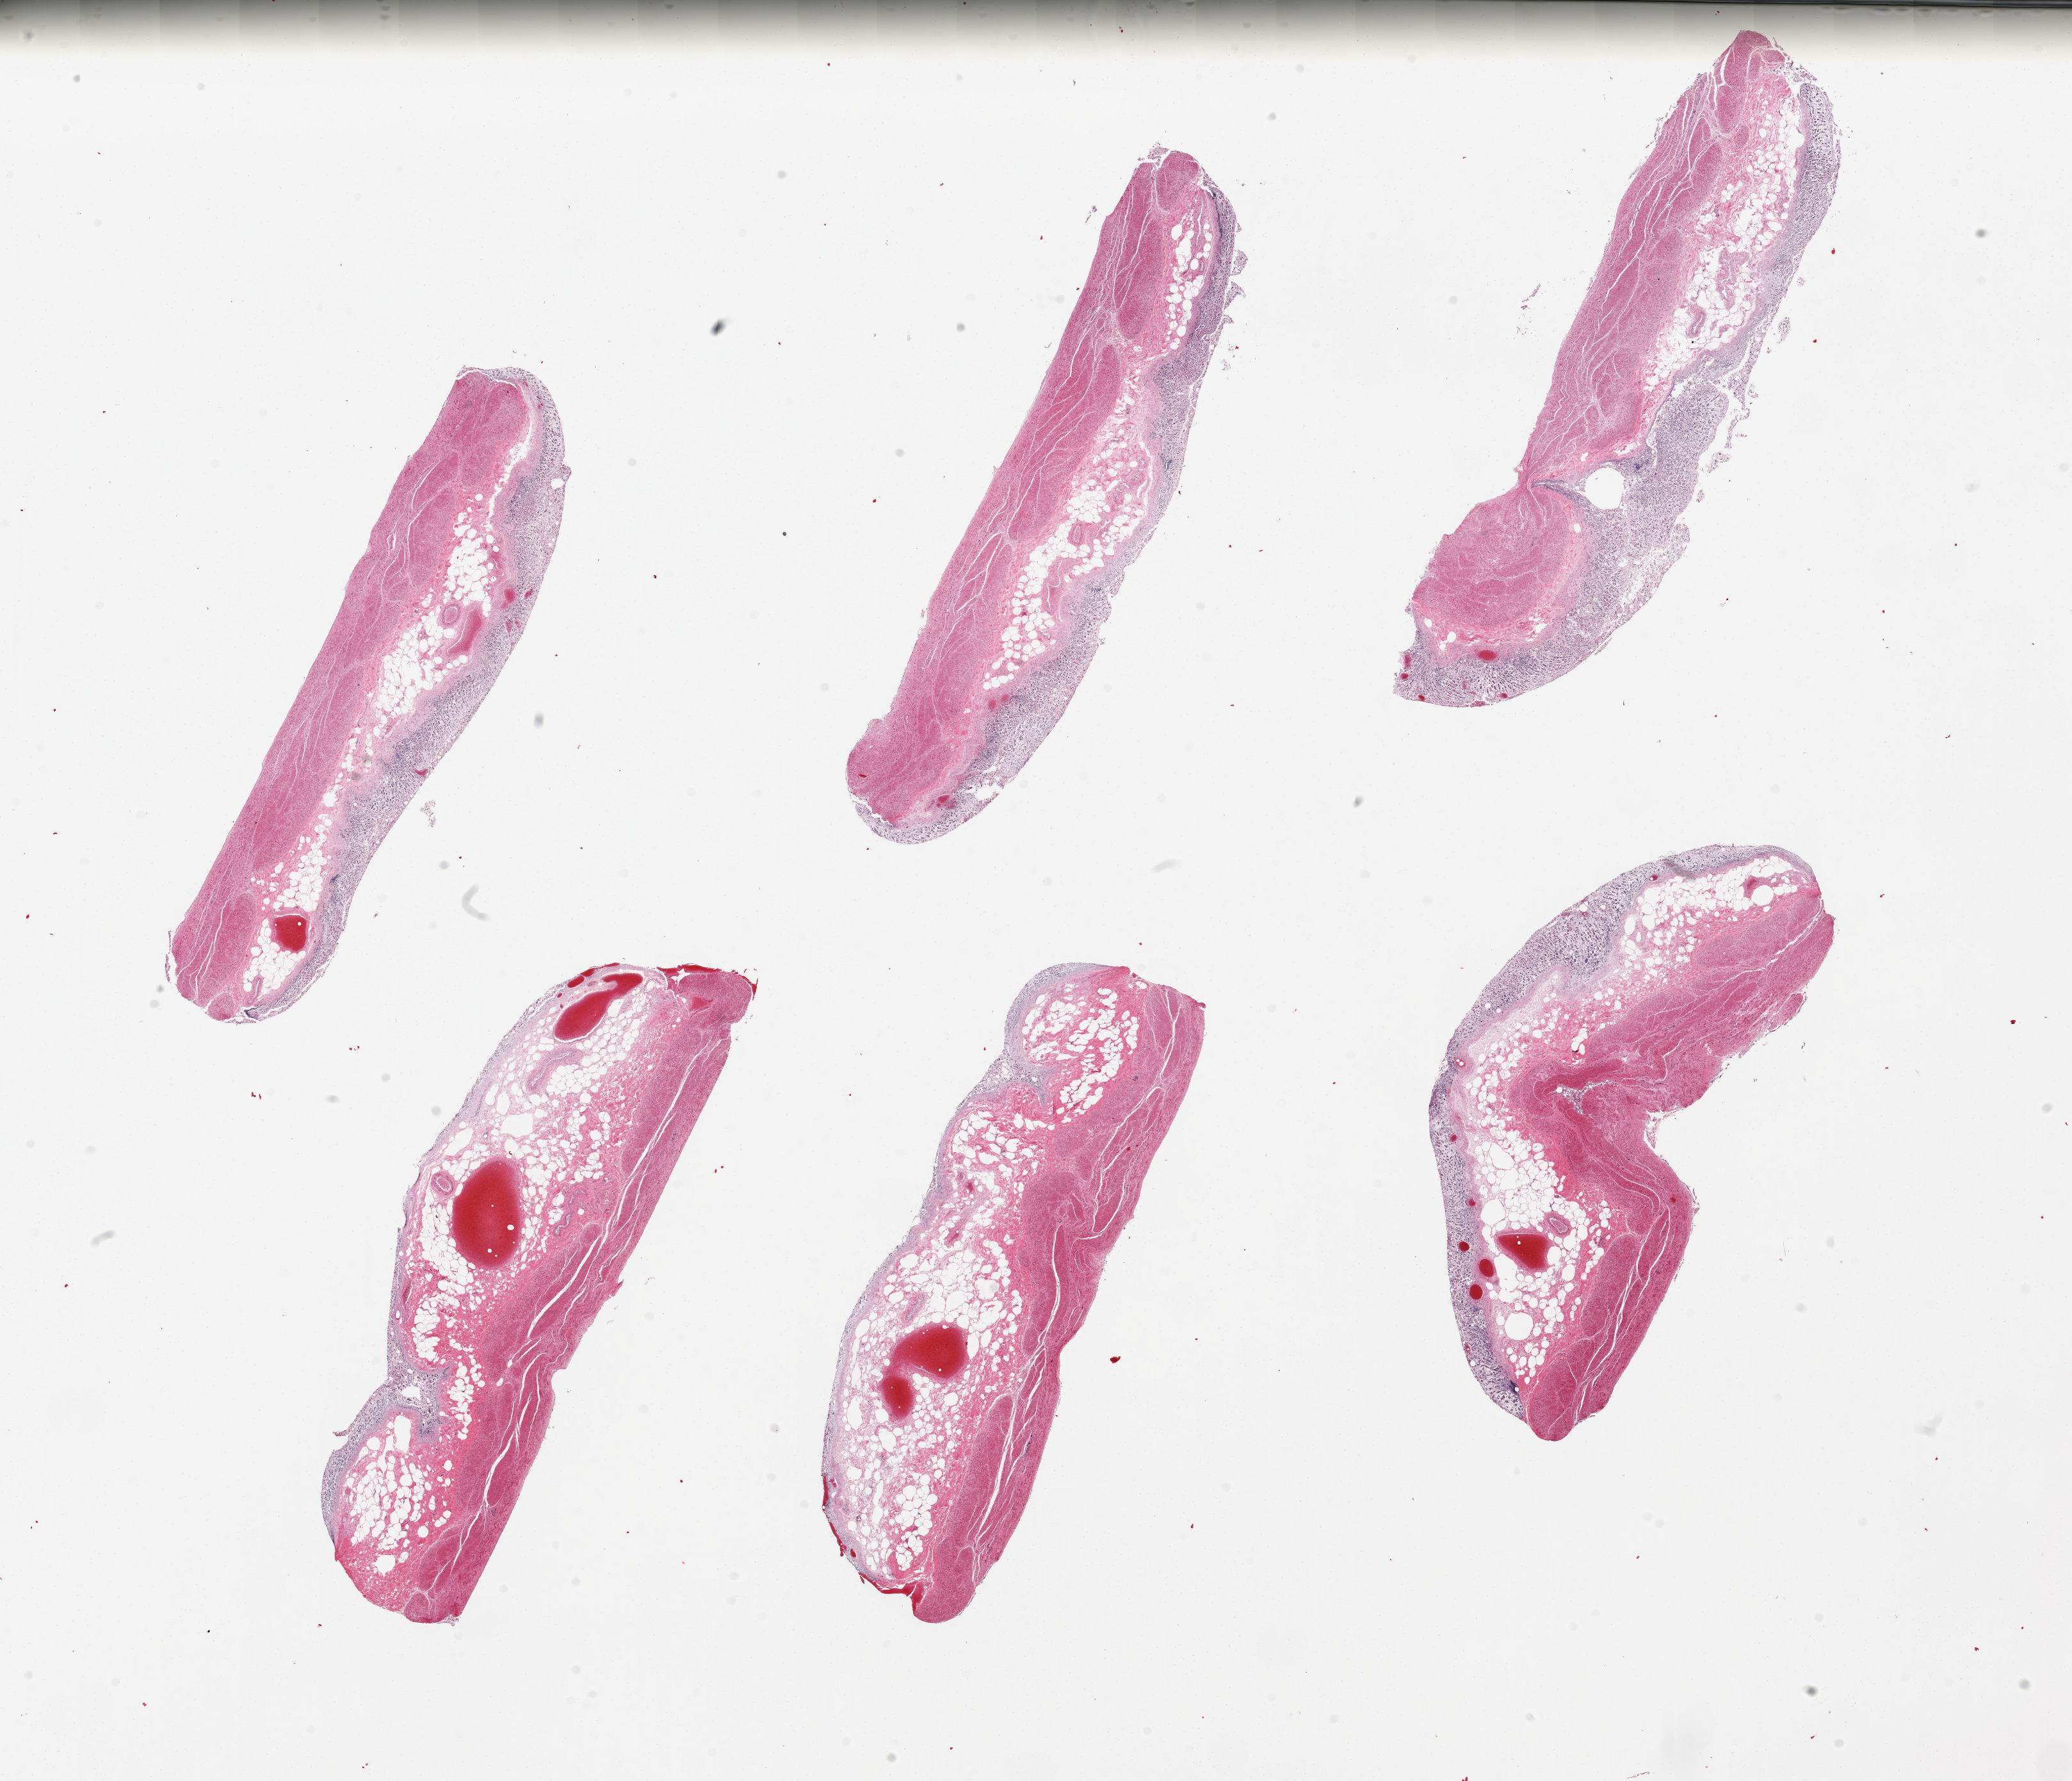
Hematoxylin and eosin (H&E) whole-slide image, brightfield, low-resolution overview of the scanned area, about 25.6 x 22.0 mm (acquisition: 20x scan); PAXgene-fixed paraffin-embedded (PFPE) section; target tissue: stomach; tissue donor sample. Donor sex: male.
Reviewer comment on this tissue sample: 6 pieces, mucosa up to ~50% thickness but badly autolyzed.